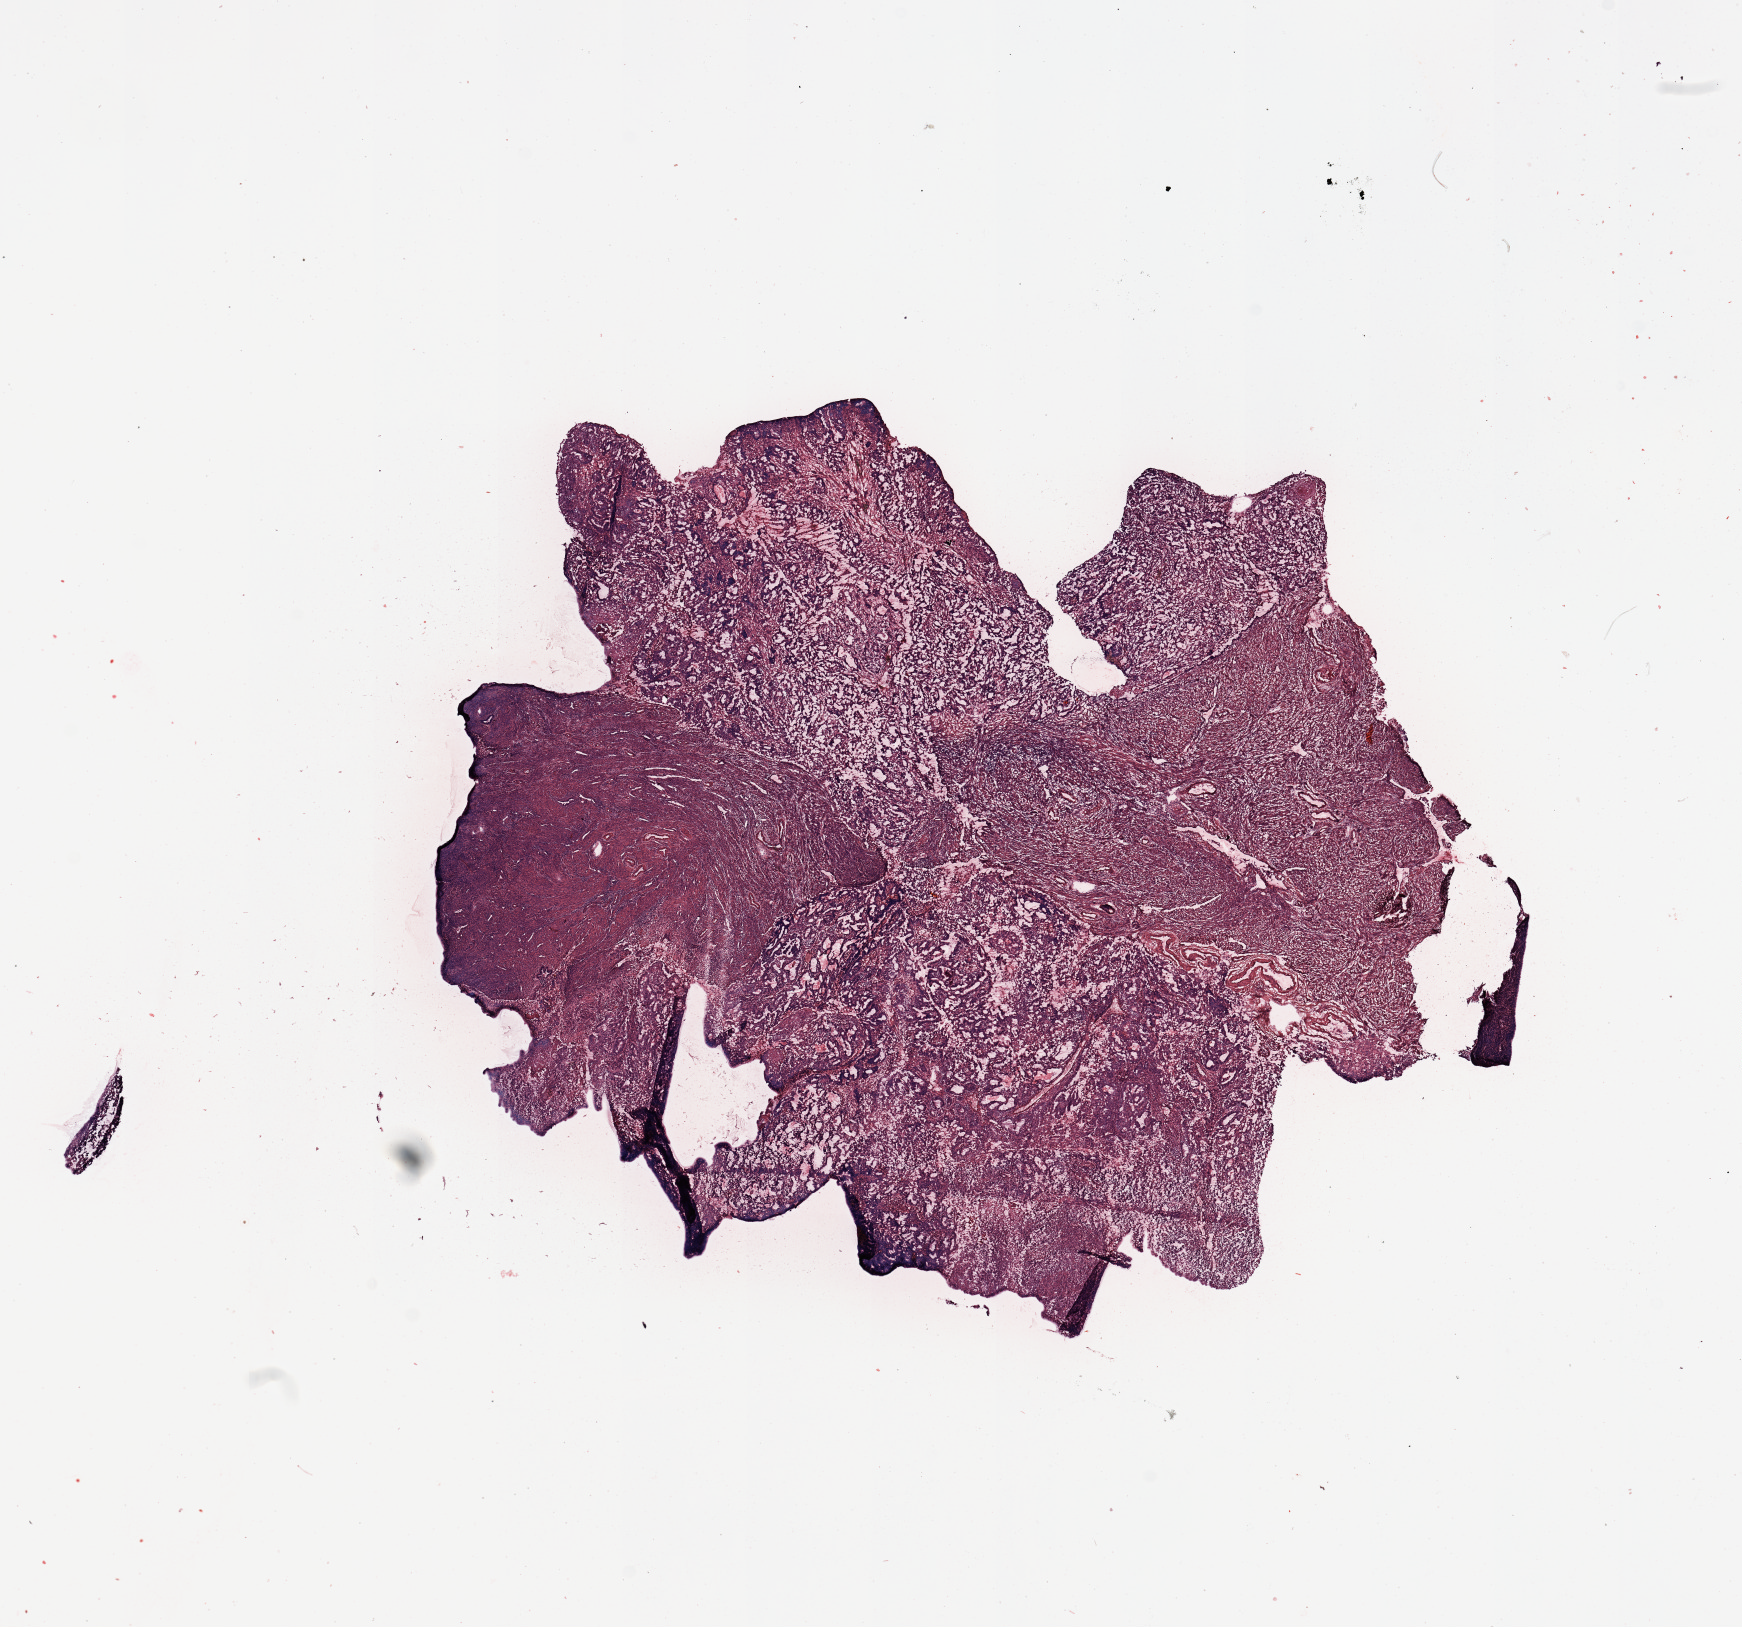
Whole-slide histology image, H&E-stained, shown as a low-resolution overview of the whole scanned area (about 13.8 x 12.9 mm), tumour tissue sample, uterus. Patient: female, age 65 years. Histologic grade: G2 (moderately differentiated).
* AJCC pathologic stage: I
* diagnosis: Endometrioid adenocarcinoma, NOS